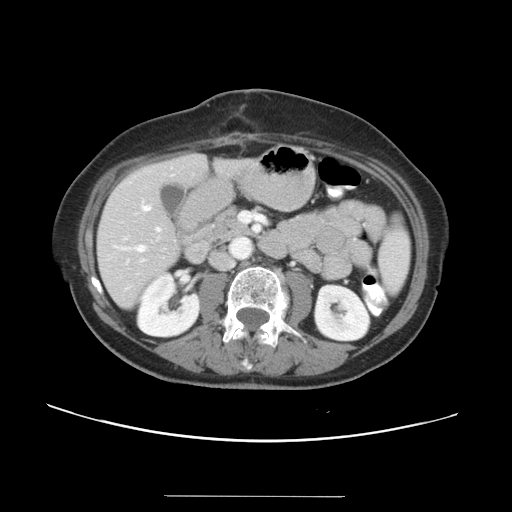
Contrast-enhanced abdominal CT, one axial slice; slice 12 of 34 in the series (ordered by position); 120 kVp; intravenous contrast given; soft-tissue window (W 400 / L 40 HU); 5 mm slice thickness; 512 × 512 image matrix, field of view 382 × 382 mm. Female patient, age 69 years. Case-level facts recorded for this patient, not image findings: diagnosis: colorectal cancer liver metastases, imaged before liver resection; multiple liver metastases: yes; largest metastasis: 1.4 cm; disease in both lobes: yes.
Outlined on this slice (expert manual segmentation):
- hepatic veins: box from (x=115, y=205) to (x=151, y=262) px
- liver: (x=98, y=154)–(x=252, y=307)
- planned liver remnant (the part of the liver to remain after resection): (x=98, y=154)–(x=252, y=307)
- portal vein (with intrahepatic branches): (x=139, y=212)–(x=265, y=250)